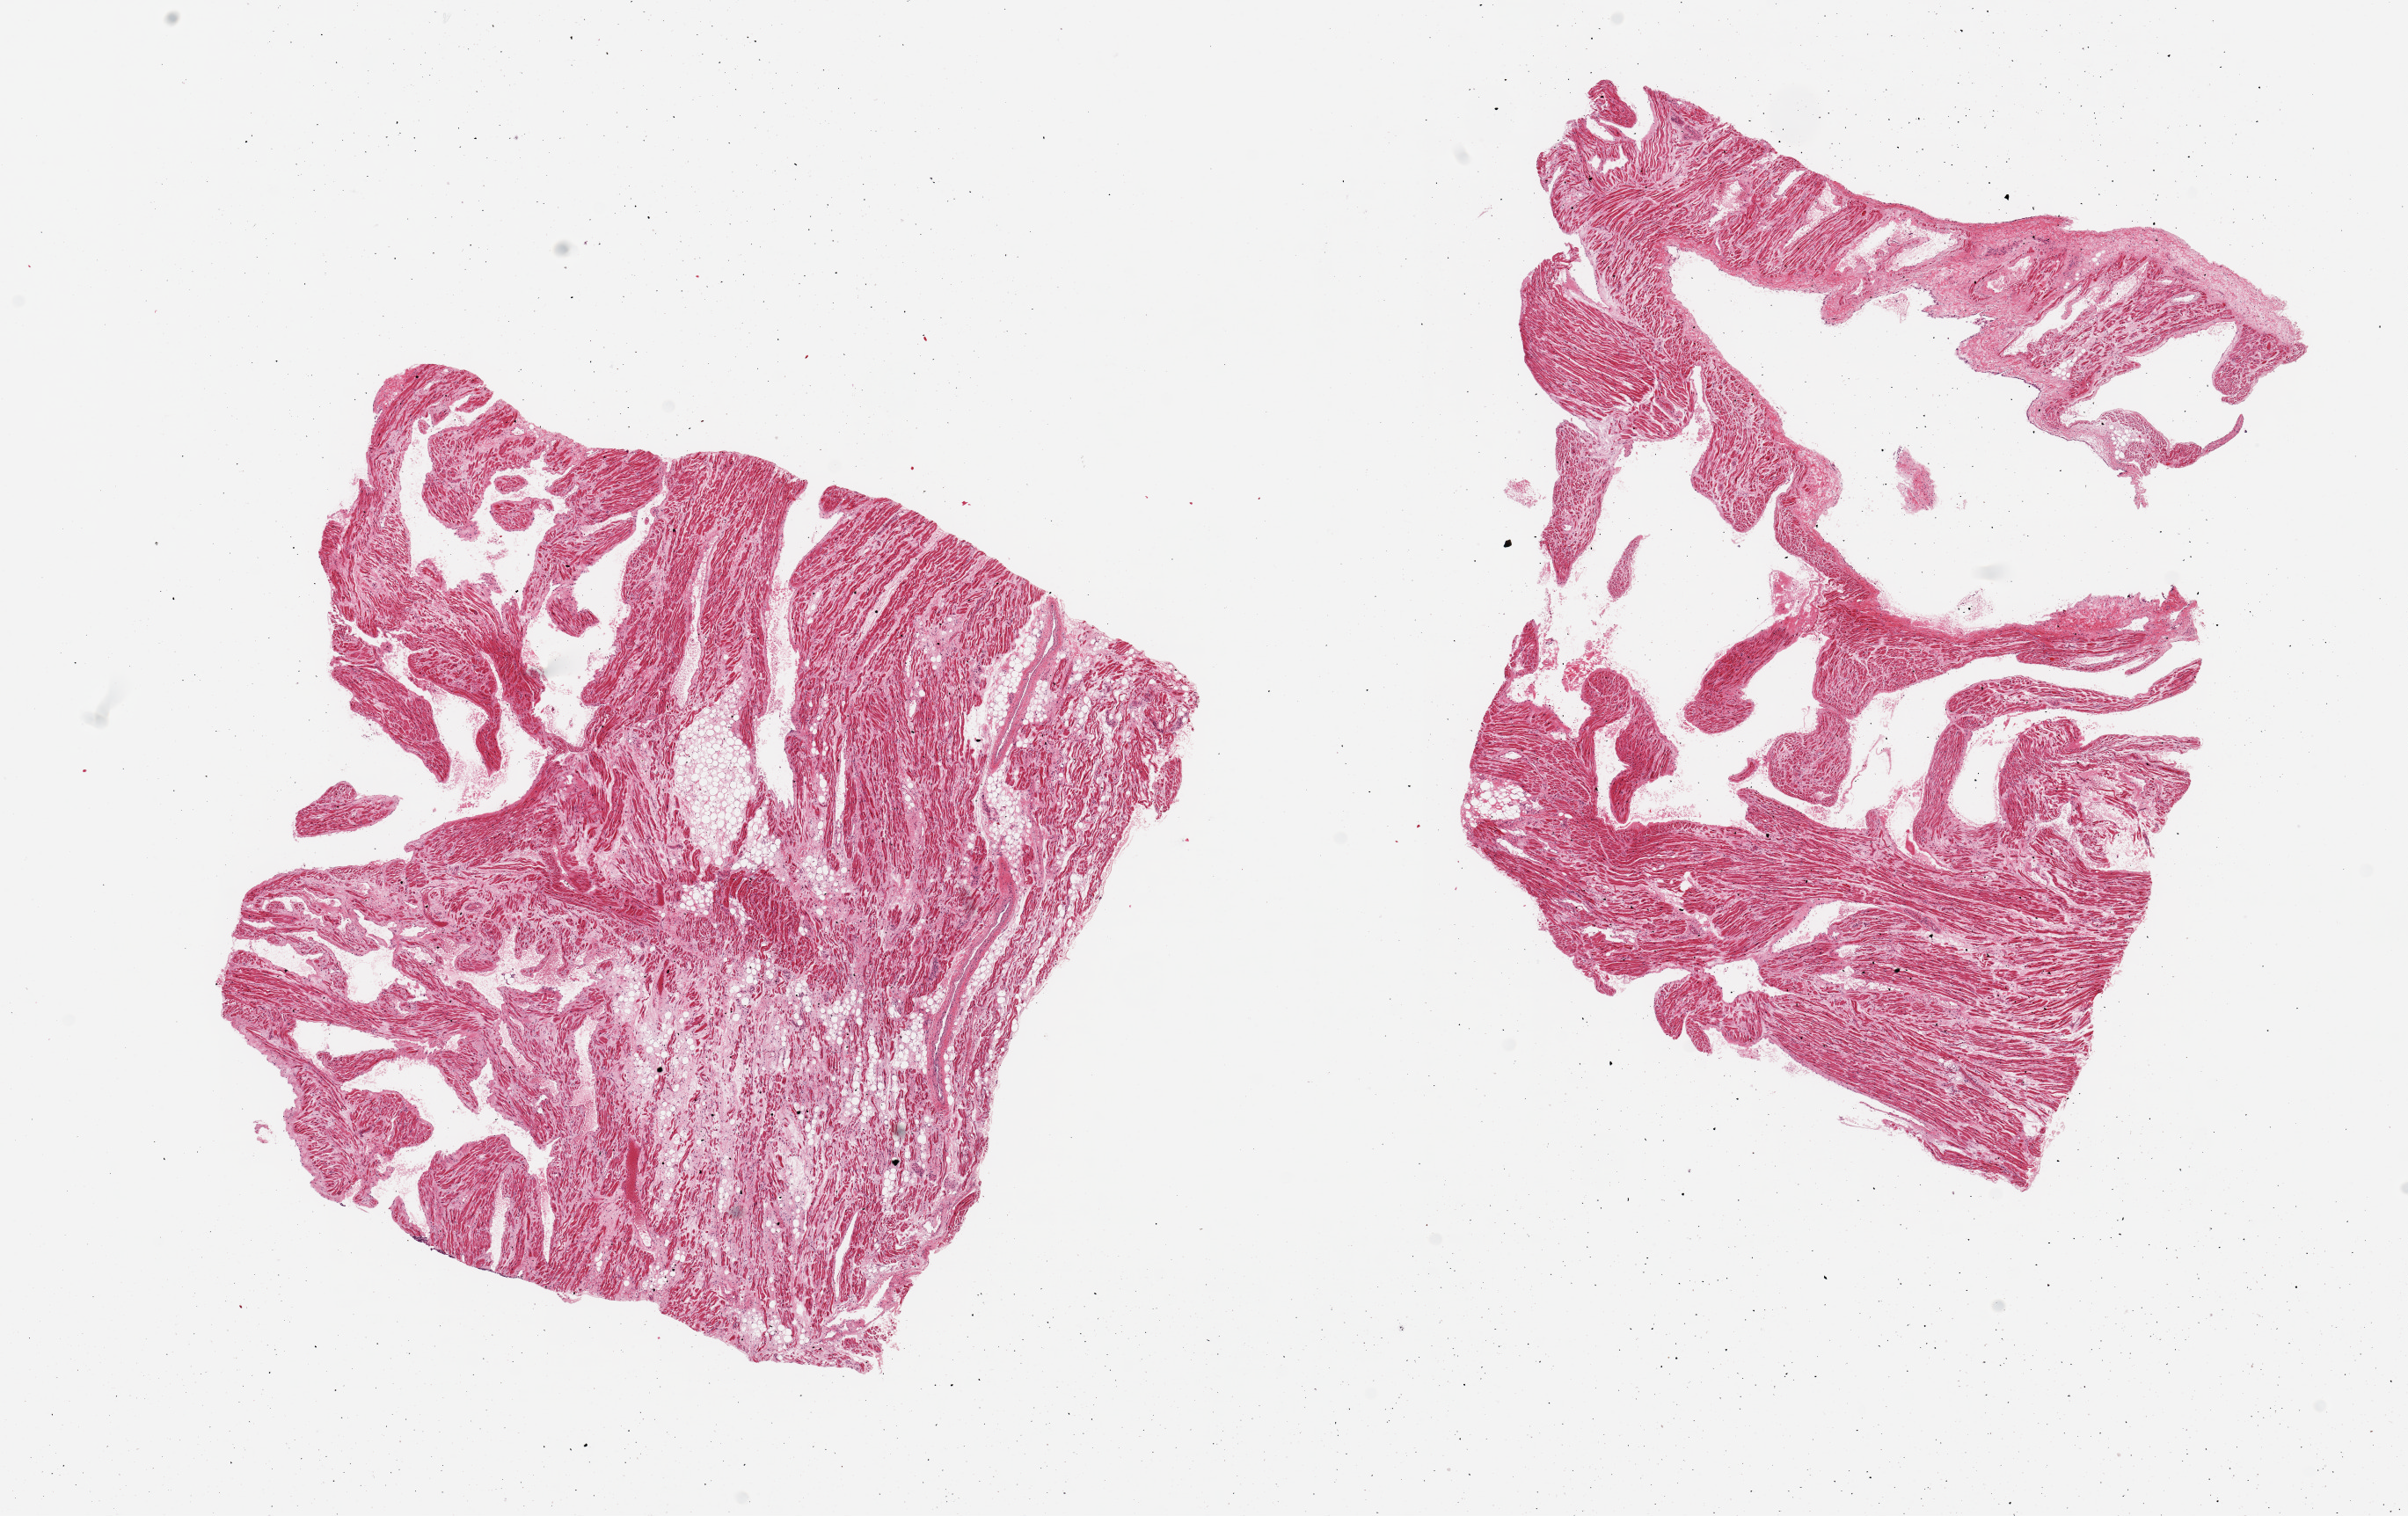
Digitized H&E-stained section — shown as a low-resolution overview of the whole scanned area (about 21.7 x 13.6 mm, acquisition: 20x scan); PAXgene-fixed paraffin-embedded (PFPE) section; section of auricular appendage (target tissue); donor tissue sample.
* reviewer comment on this tissue sample: 2 pieces; 30% fibrofatty content on 1 piece